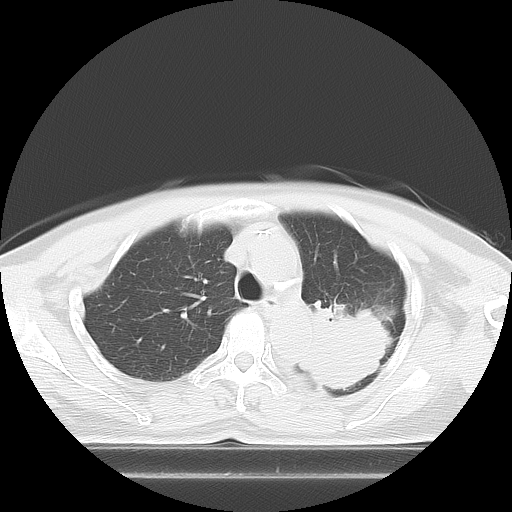
Chest CT, one axial slice. Slice 7 of 21 in the series (ordered by position). 120 kVp. Lung window (W 1500 / L -600 HU). 5 mm slice thickness. 512 × 512 image matrix, field of view 350 × 350 mm. Female patient, age 74 years. From the clinical record (not read from this slice): clinical TNM (as recorded): T3 N1 M1c; histopathological grade: G3.
Structures marked on this image (rectangle marked by the reading radiologist):
- lung tumour (recorded histology: small cell carcinoma): box from (x=288, y=293) to (x=405, y=391) px